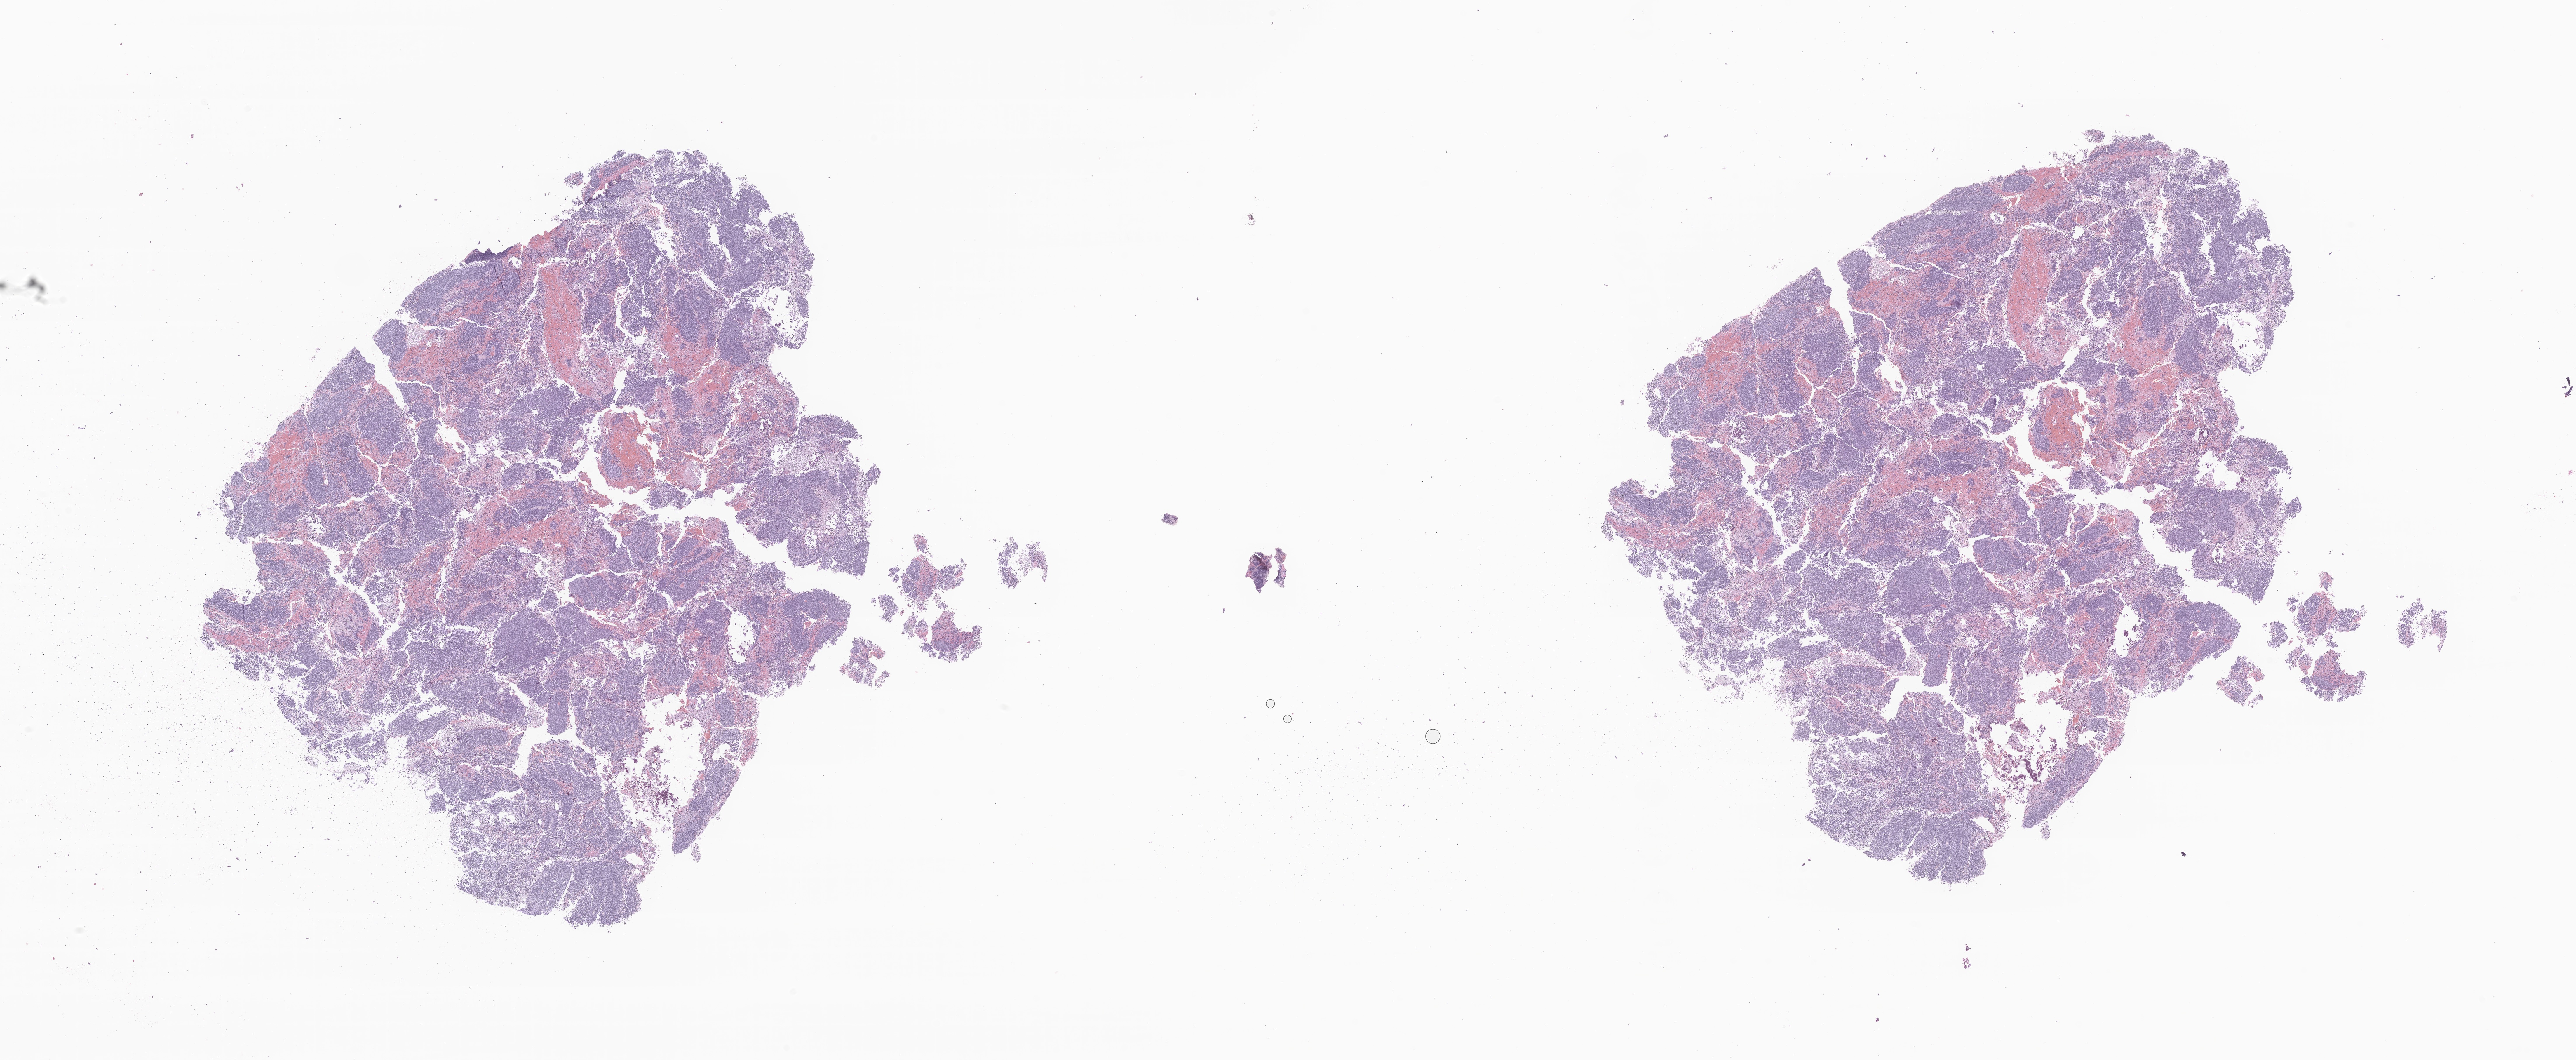
Whole-slide image, hematoxylin and eosin (H&E) stain of tumor tissue from the pineal gland, whole scanned area (about 37.2 x 15.3 mm) shown as a low-resolution overview, FFPE section. Patient: female, age 63 months (5 years 3 months).
Recorded diagnosis: Pineoblastoma.